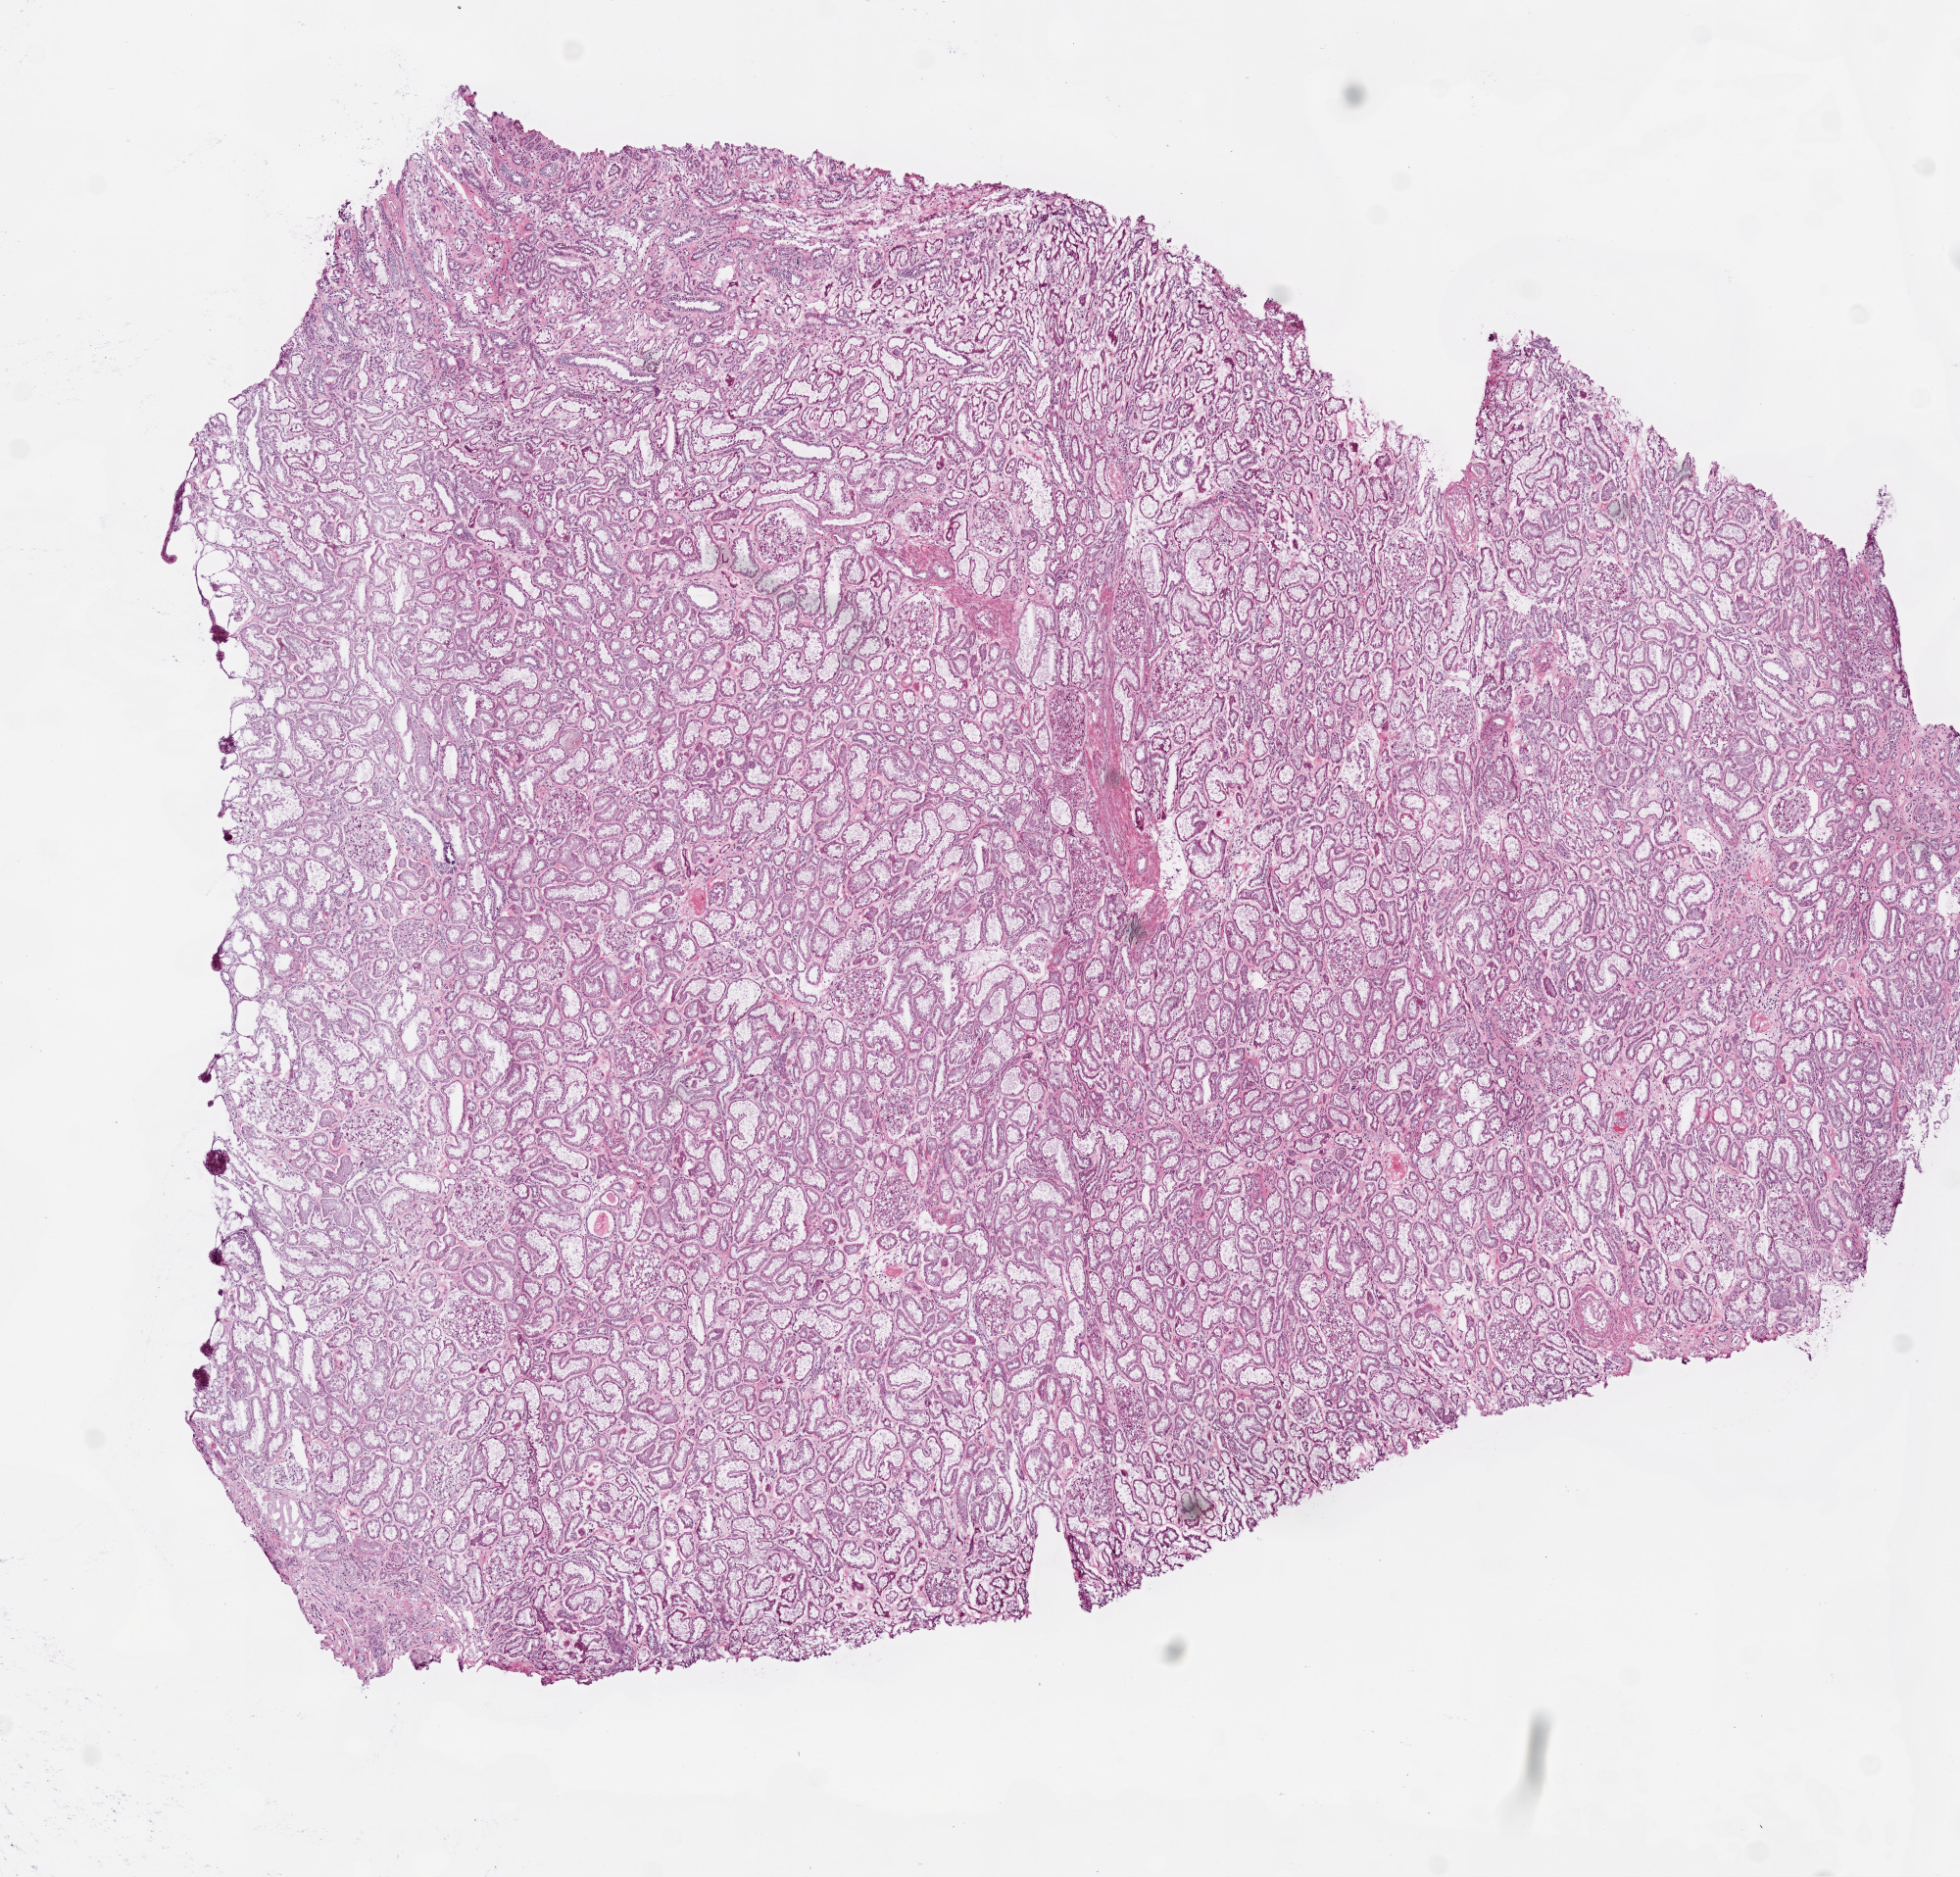
H&E-stained whole-slide image — low-resolution overview of the scanned area, about 8.0 x 7.7 mm (from a 20x scan), frozen section from the top of the tissue portion, sample: solid tissue normal (non-tumour tissue), kidney. Patient: male, age at initial diagnosis 64 years.
• this section: solid tissue normal sample (biorepository sample class)
• patient diagnosis: Papillary adenocarcinoma, NOS